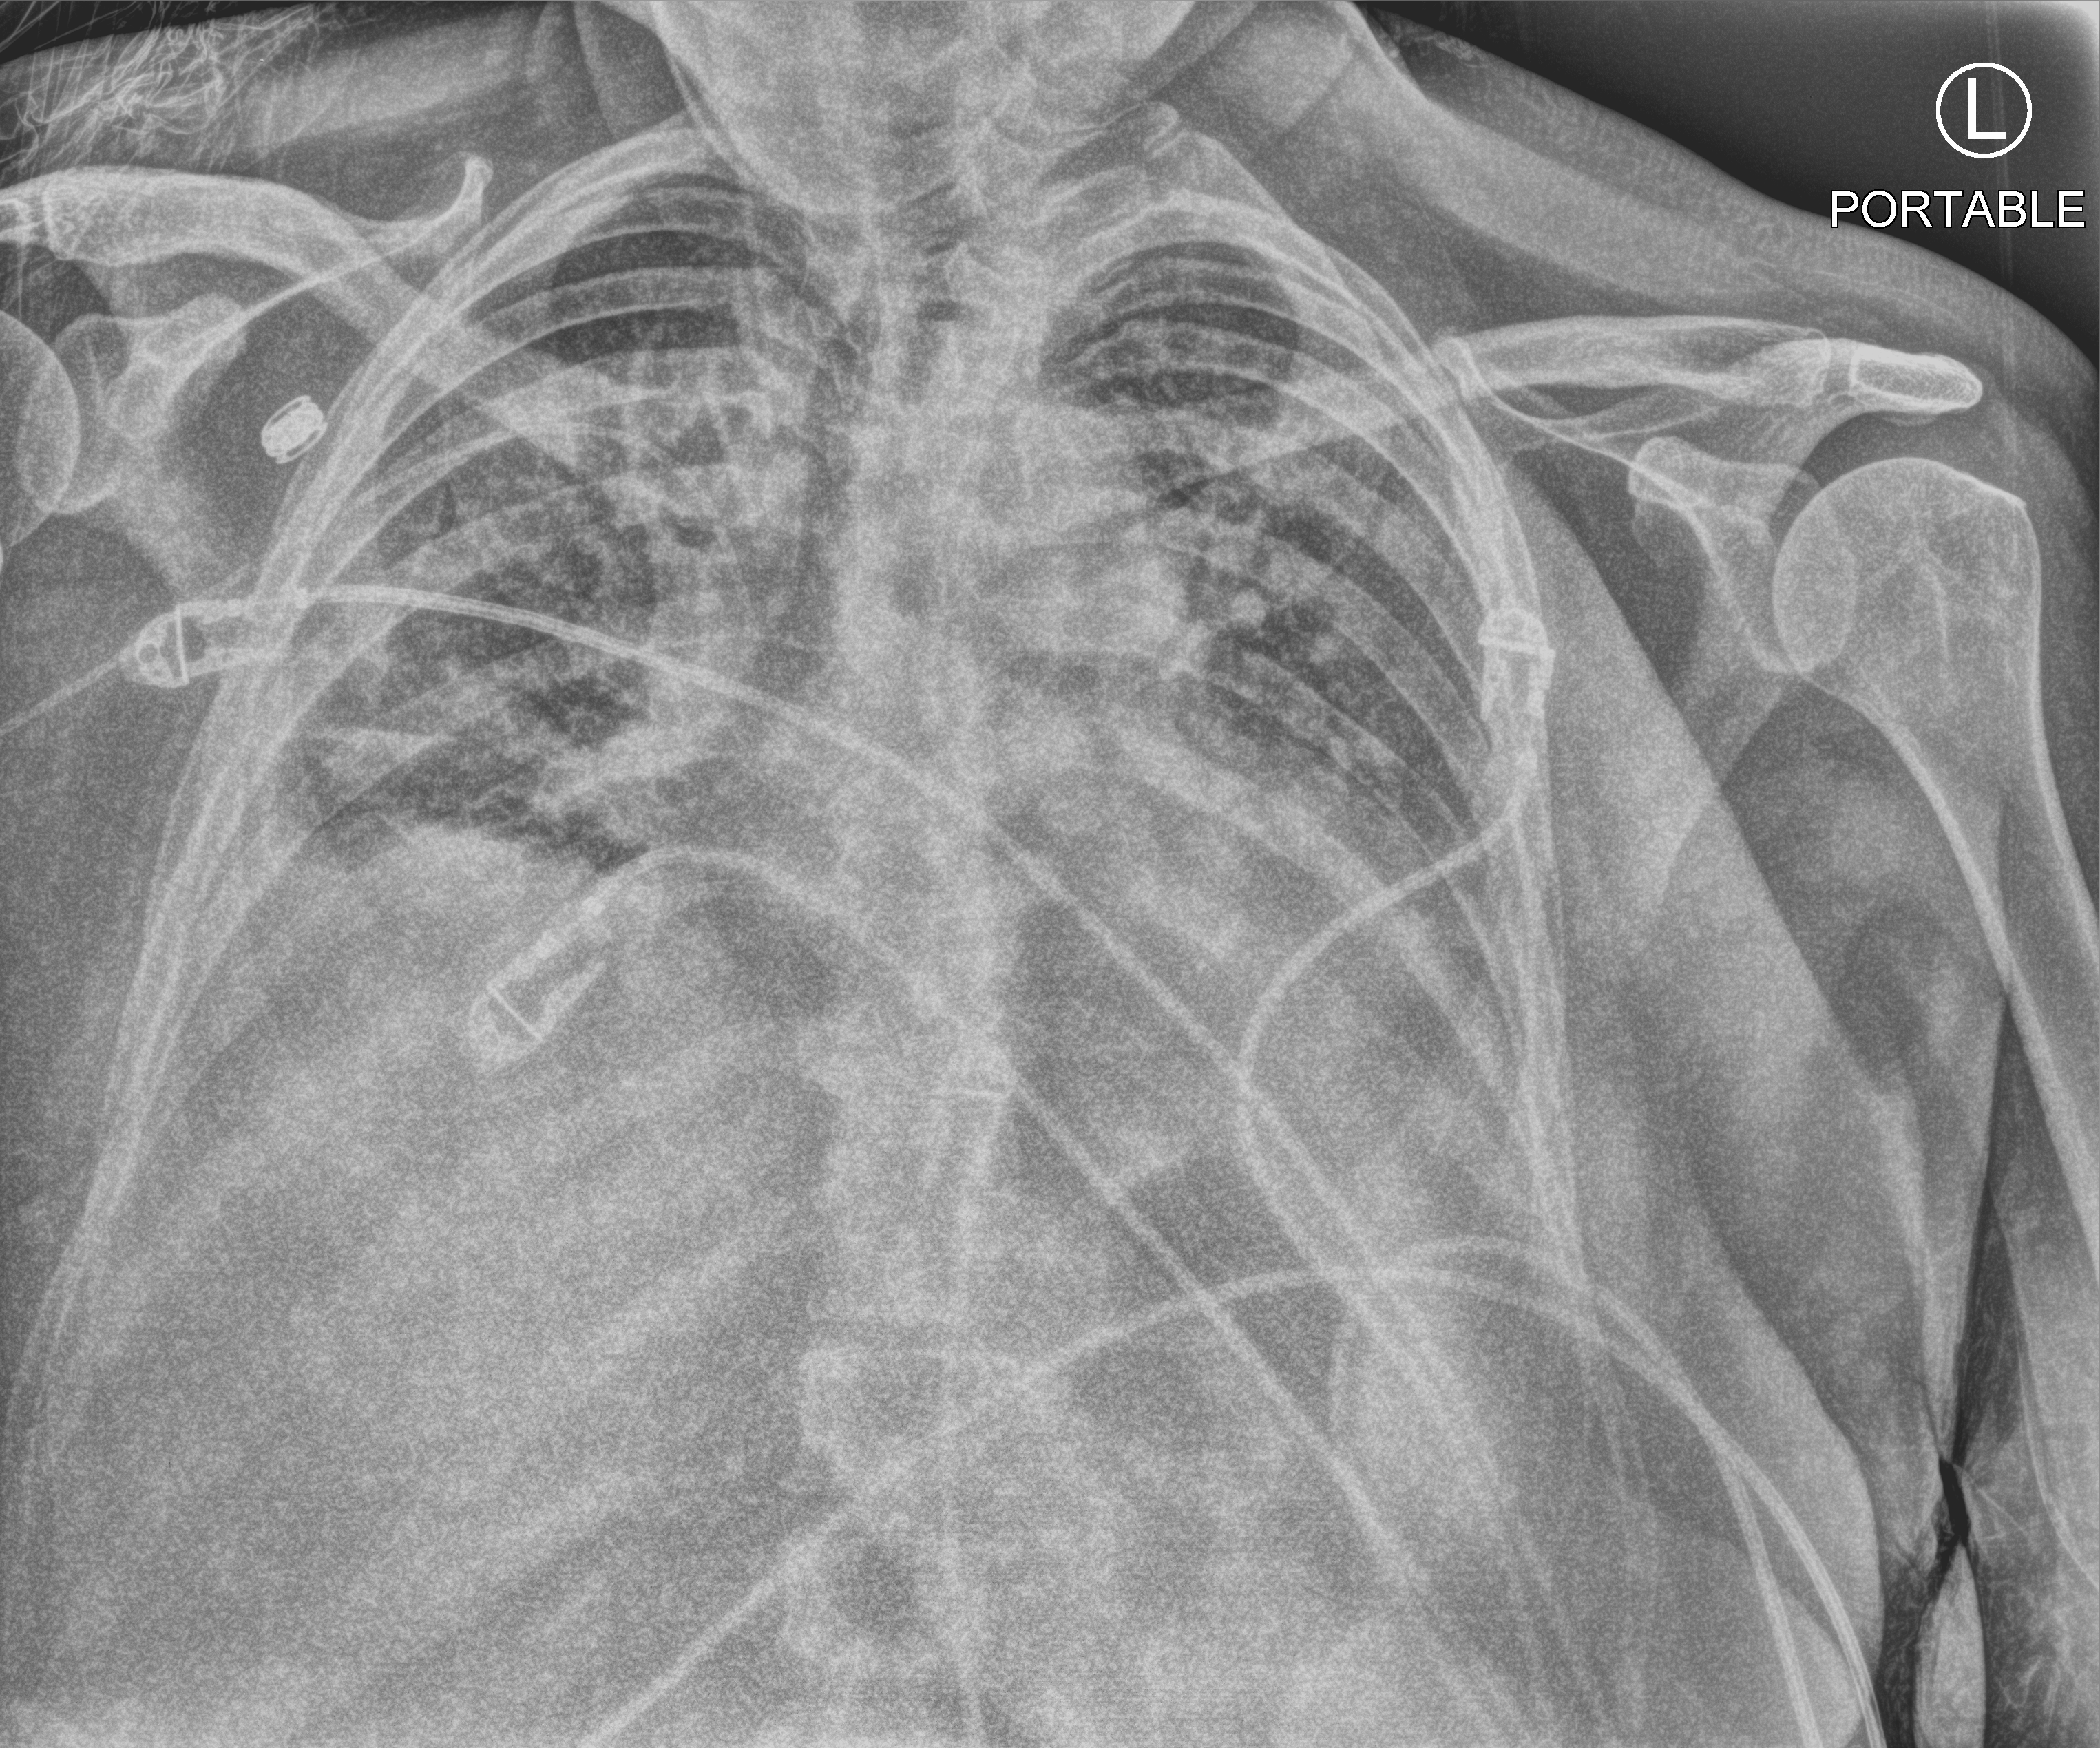
Portable chest radiograph, anteroposterior (AP) projection. Female patient hospitalised with COVID-19, age 60–74 years.
From the hospital-stay record, not from the radiograph (when in the stay this image was taken is not recorded): mechanically ventilated during this hospital stay: yes; admitted to intensive care during this hospital stay: yes.